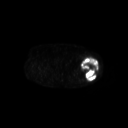
FDG PET of an extremity soft-tissue mass (from a PET/CT study), one axial slice. 3.27 mm slice thickness. 128 × 128 image matrix, field of view 700 × 700 mm. Patient: female, 62 years. Case-level facts recorded for this patient, not image findings: histological type: undifferentiated – high grade; grade: high; site of the primary tumour: left thigh.
Structures marked on this image (expert contour drawn on MRI and transferred to this co-registered scan by the dataset authors):
- gross tumour volume including surrounding oedema: bounding box (x1, y1, x2, y2) in pixels: (81, 56, 99, 81)
- gross tumour volume (mass): (81, 56, 99, 81)